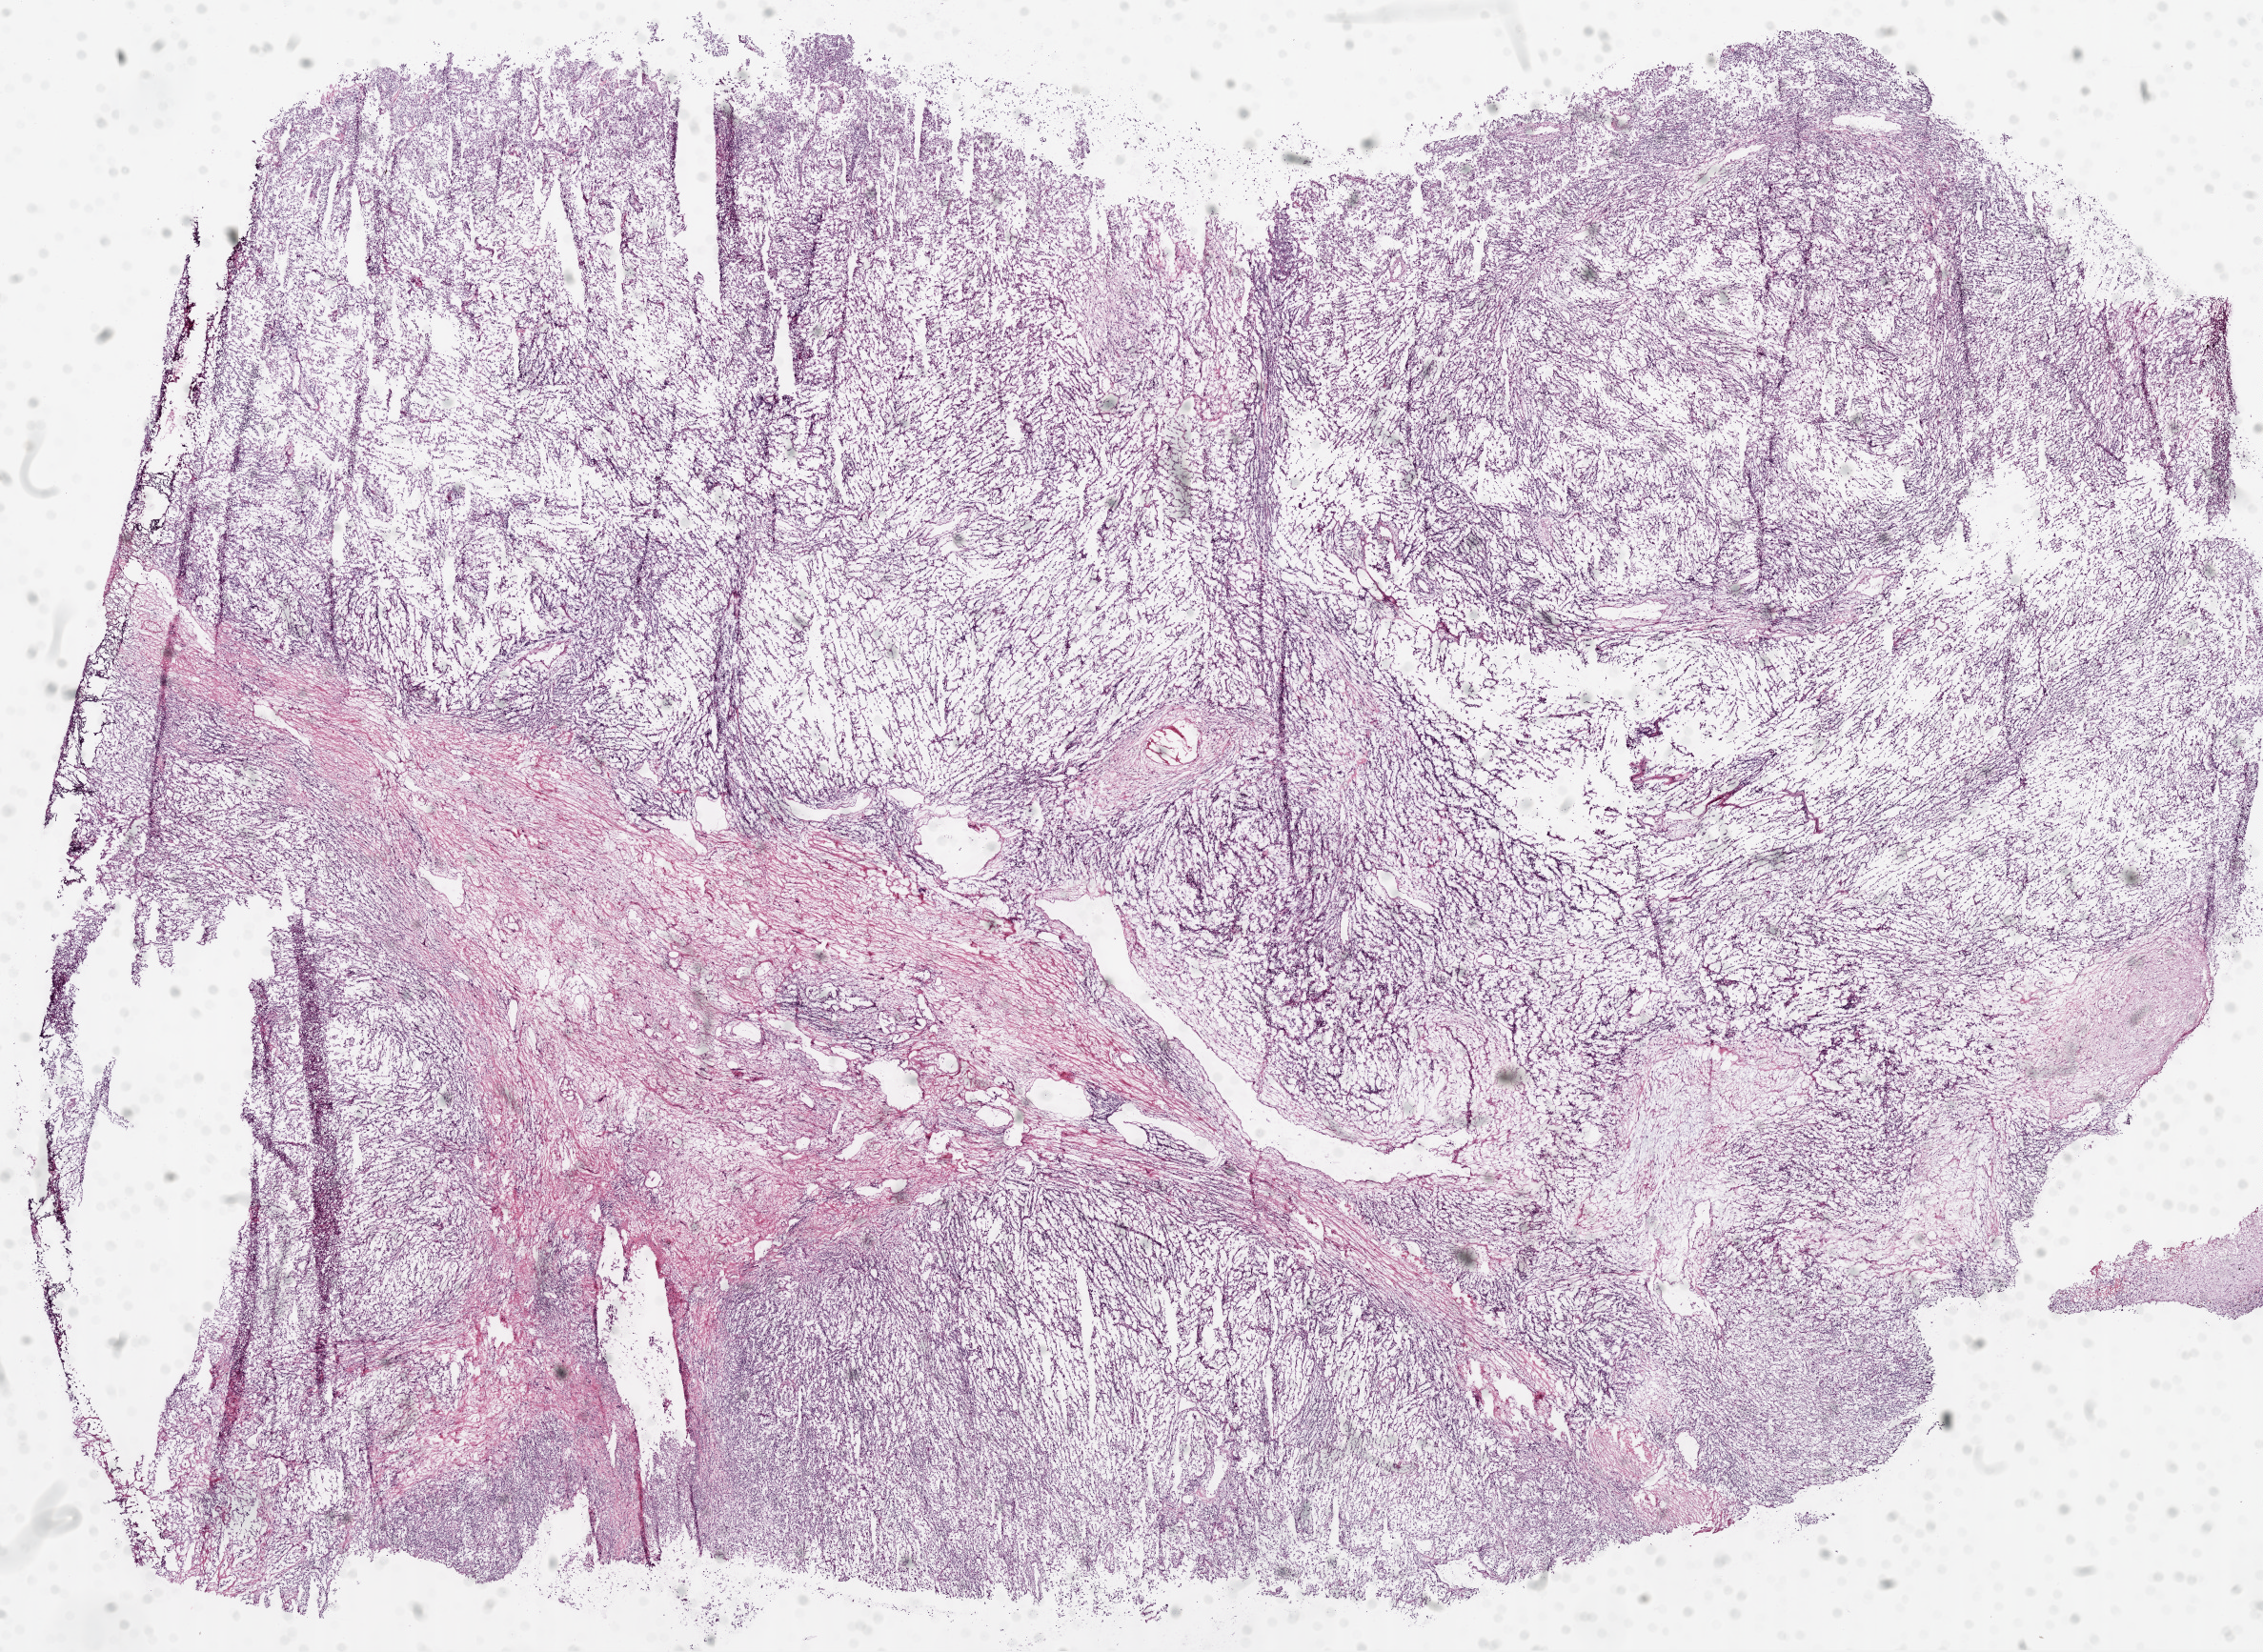
Whole-slide histology image, H&E-stained, whole scanned area (about 19.1 x 13.9 mm, from a 20x scan) shown as a low-resolution overview, frozen section, primary tumour sample from the kidney. Female, age 46 years at initial diagnosis. Histologic grade: G4 (undifferentiated). Pathologist review of this section (percent, as recorded): tumour cells 80%, tumour nuclei 80%, normal cells 0%, stromal cells 20%, necrosis 0%.
- AJCC pathologic stage: IV
- laterality: right
- diagnosis: Clear cell adenocarcinoma, NOS